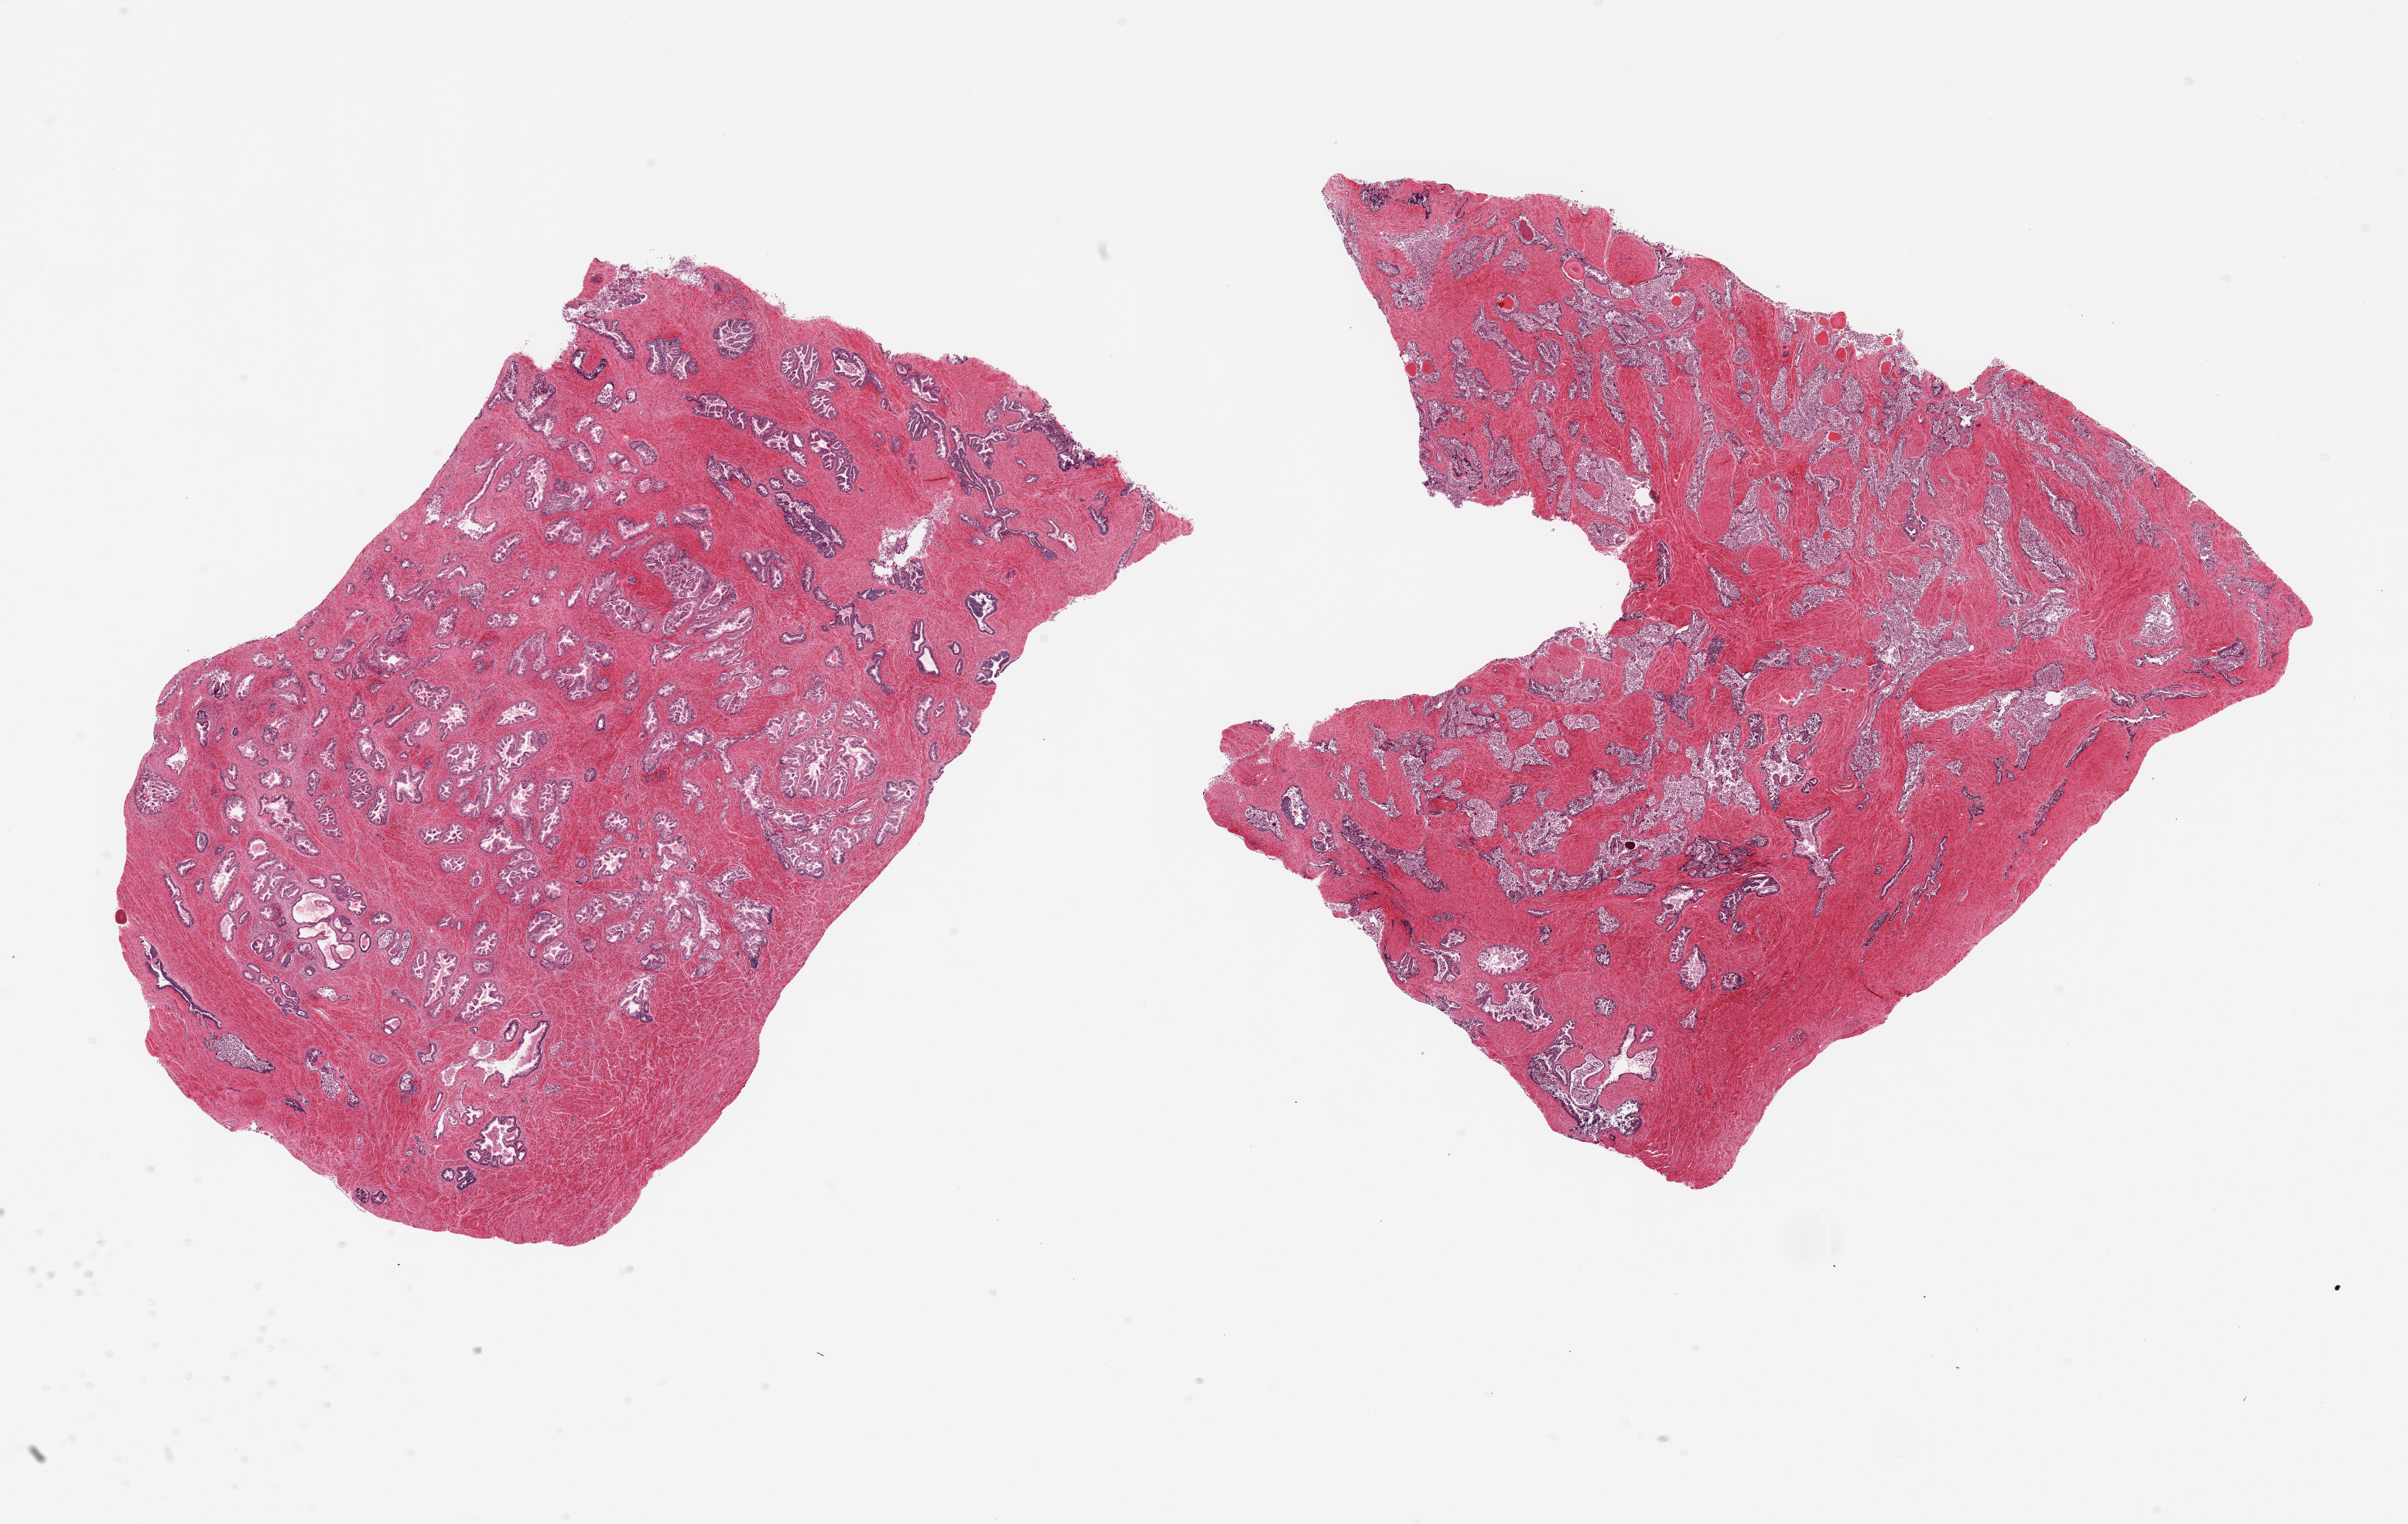
Whole-slide image, hematoxylin and eosin (H&E) stain — shown as a low-resolution overview of the whole scanned area (about 24.6 x 15.6 mm, slide scanned at 20x), PAXgene-fixed, paraffin-embedded tissue, sampled site (target tissue): prostate, donor tissue sample. Donor: male.
Reviewer comment on this tissue sample: 2 pieces; fairly well preserved fibromuscular stroma and prostatic glandular component in 1 piece; not well preserved glands in the other.